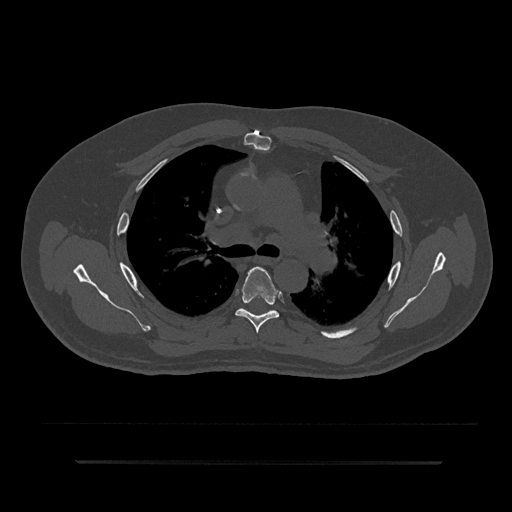
CT including the spine, one axial slice. Bone window (W 1800 / L 400 HU). 0.5 mm slice thickness. 512 × 512 image matrix, field of view 464 × 464 mm. Patient: male, 59 years. From the clinical record (not read from this slice): primary cancer: bile ducts; vertebrae with lytic lesions (as recorded): T10.
Outlined on this slice (semi-automatic segmentation, software-assisted and operator-edited):
- T5 vertebra: bounding box <235,267,280,333> (left, top, right, bottom; pixels)
- T6 vertebra: <243,308,247,311>